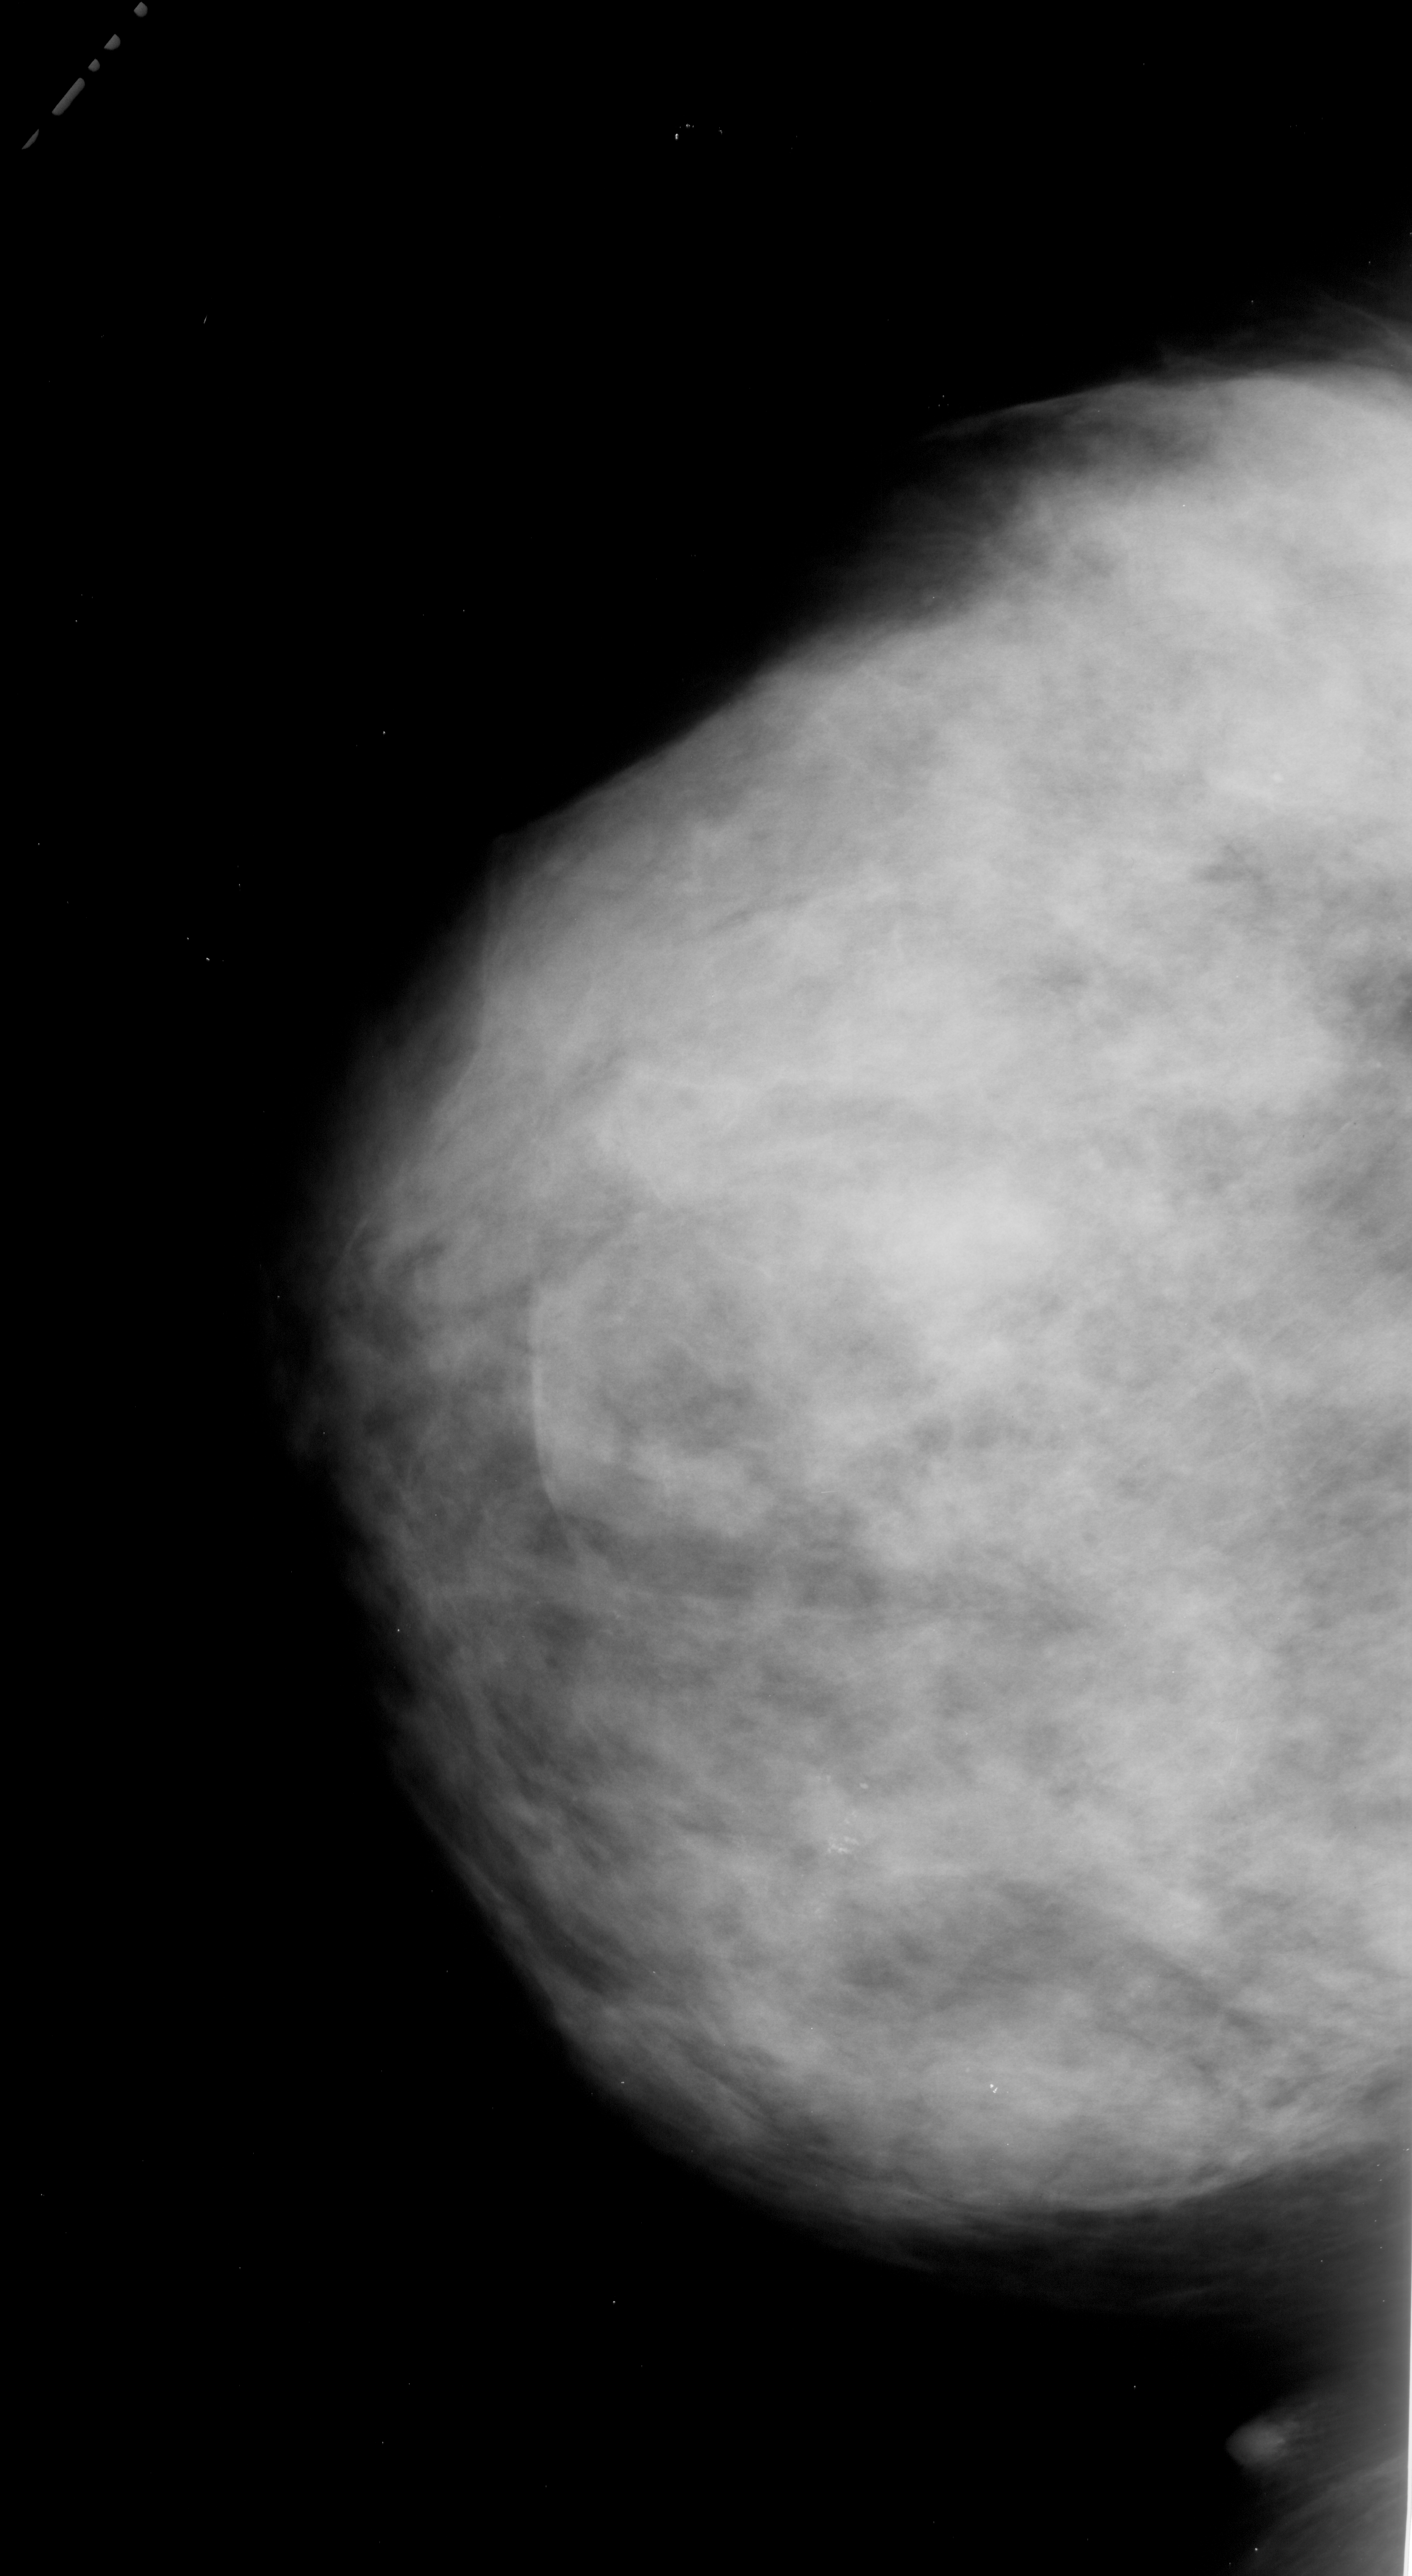
Digitized screen-film mammogram; left breast; CC view; 1412 × 2576 image matrix.
Expert-marked regions of interest on this film, with their recorded descriptors:
- calcifications, morphology pleomorphic, distribution clustered; BI-RADS assessment category 4; subtlety rating 3 on a 1 (subtle) to 5 (obvious) scale; pathology result (as recorded, not read from the image): malignant: bounding box <704,1745,893,1954> (left, top, right, bottom; pixels)